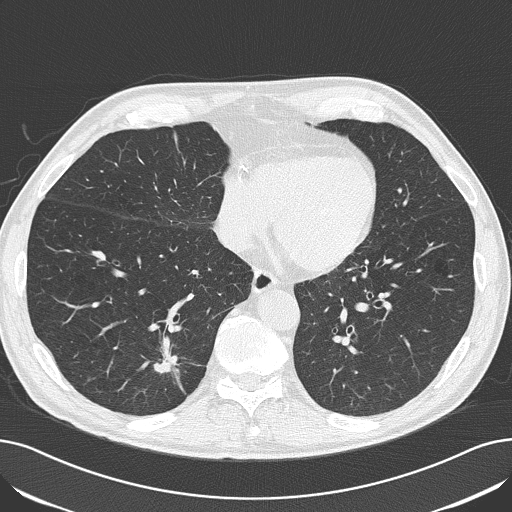
Low-dose screening chest CT, one axial slice. Position 61 of 182 along the scan axis. 120 kVp. Lung window (W 1500 / L -600 HU). 2 mm slice thickness. 512 × 512 image matrix, field of view 368 × 368 mm.
Annotated regions visible in this slice (manually delineated by an expert):
- lesion 1 (tumor, lower lobe of right lung): bounding box <154,354,179,375> (left, top, right, bottom; pixels)